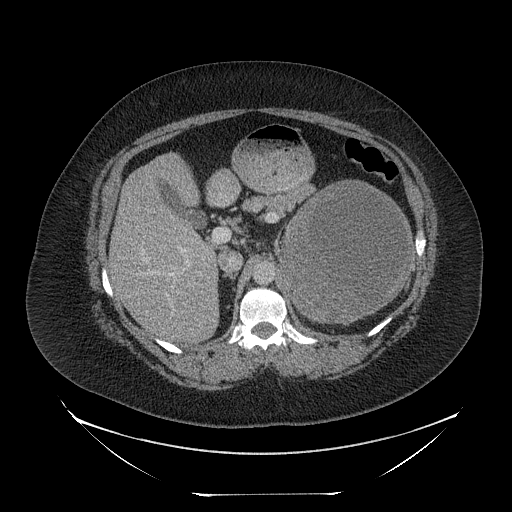
Contrast-enhanced abdominal CT, one axial slice; slice 147 of 205 in the series (ordered by position); reconstruction kernel STANDARD; 120 kVp; intravenous contrast given; soft-tissue window (W 400 / L 40 HU); 512 × 512 image matrix, field of view 500 × 500 mm. Female patient, age 53 years. From the clinical record (not read from this slice): diagnosis: adrenocortical carcinoma; tumour side: left adrenal; tumour size at pathology: 17 cm.
Structures marked on this image (semi-automatically segmented with operator editing):
- mass: bounding box [x1, y1, x2, y2] px = [283, 183, 412, 320]